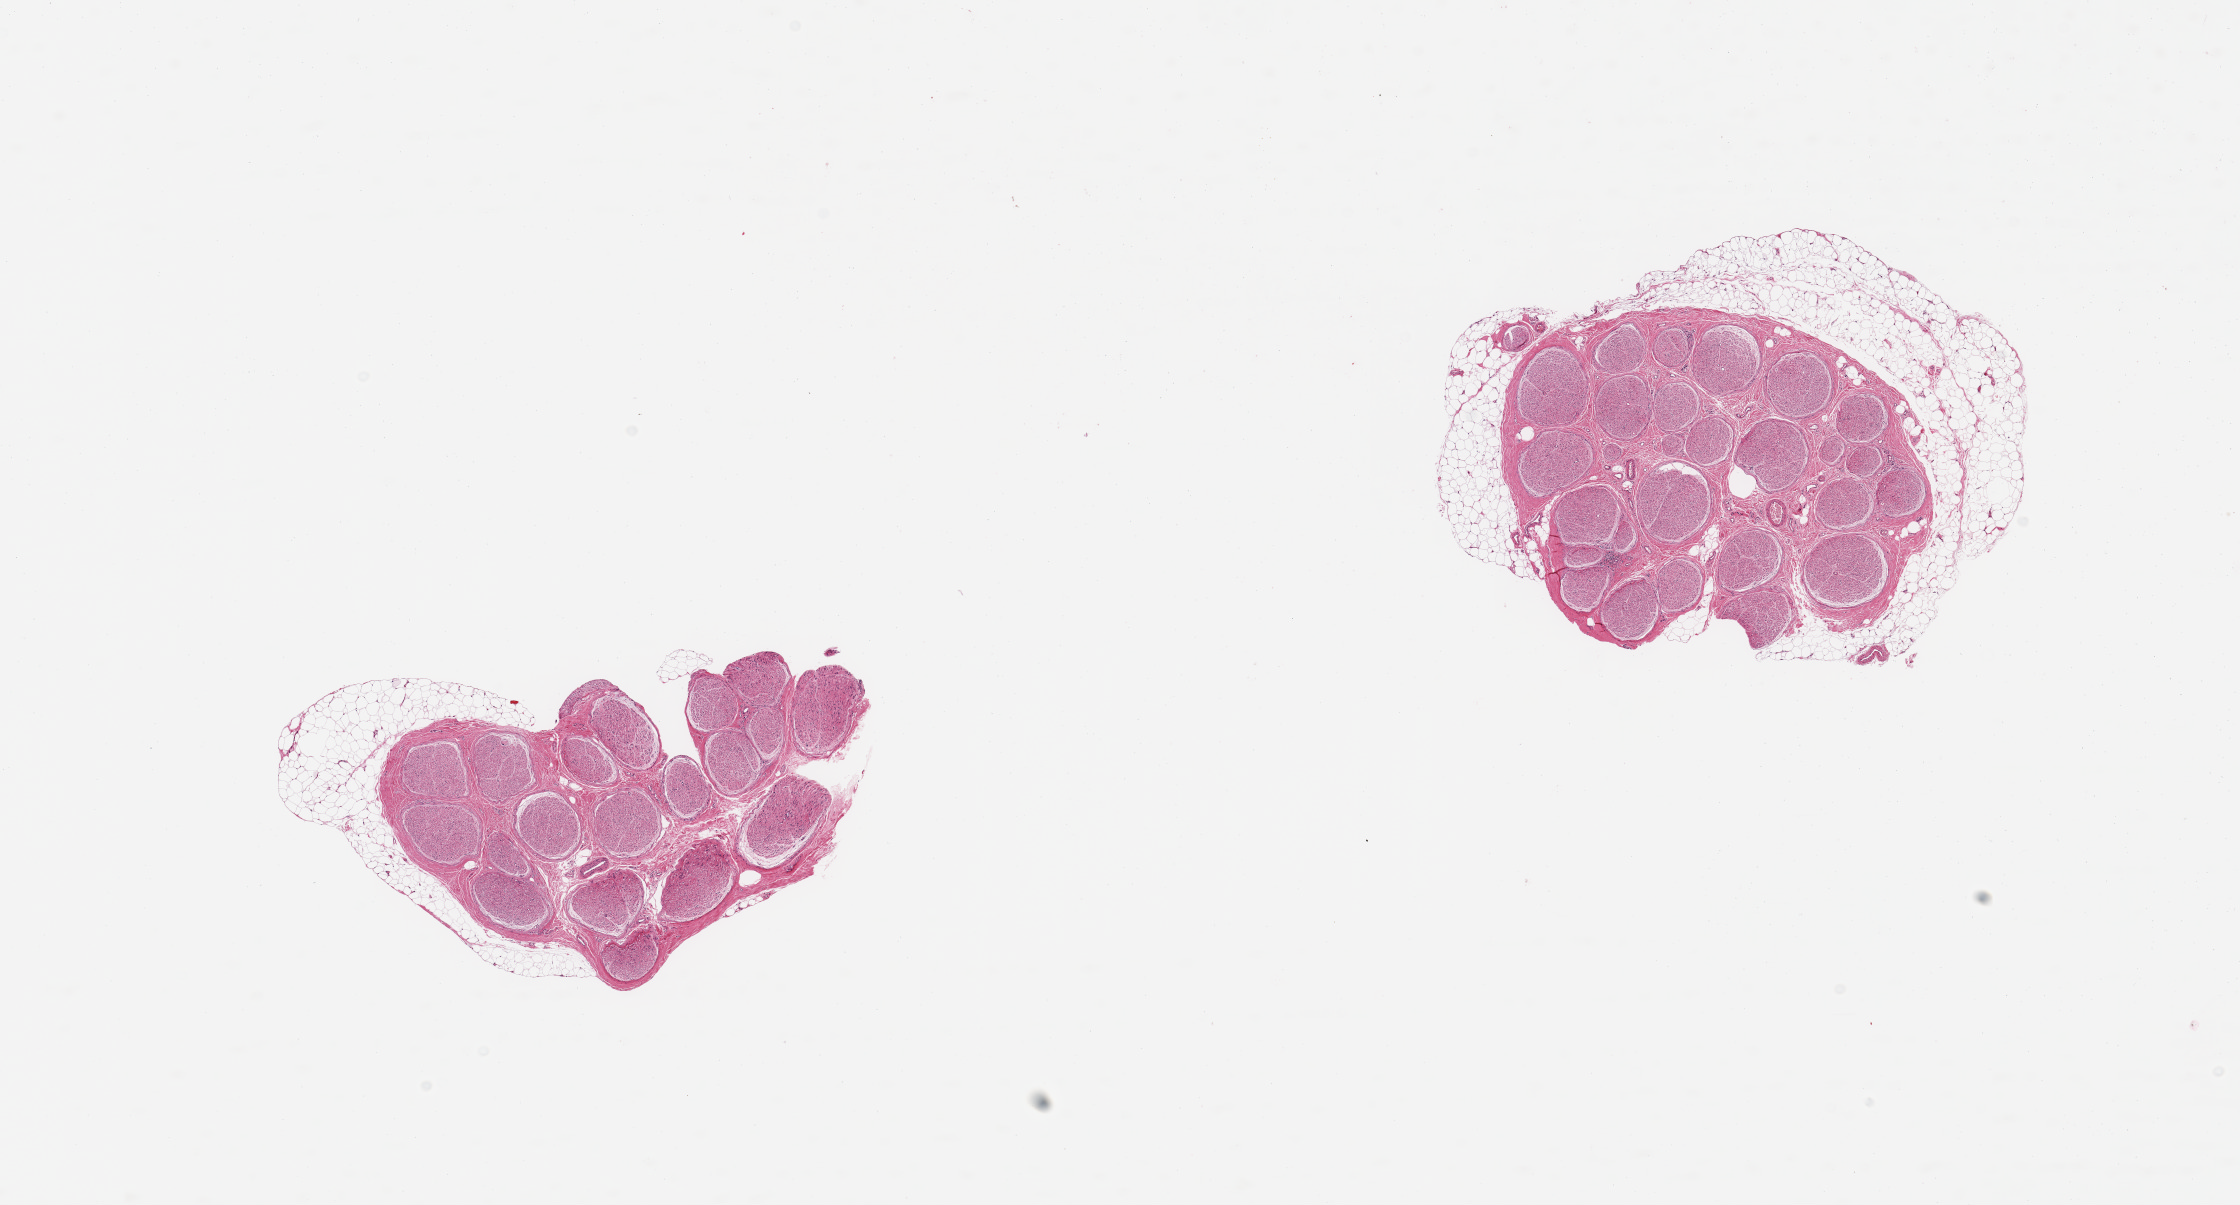
Hematoxylin and eosin (H&E) whole-slide image — low-resolution overview of the scanned area, about 17.7 x 9.5 mm (slide scanned at 20x); PAXgene-fixed paraffin-embedded (PFPE) section; section of tibial nerve (target tissue); tissue donor sample. Donor: male.
Pathologist's review note for this sample: 2 pieces, adherent fat up to ~0.8mm.